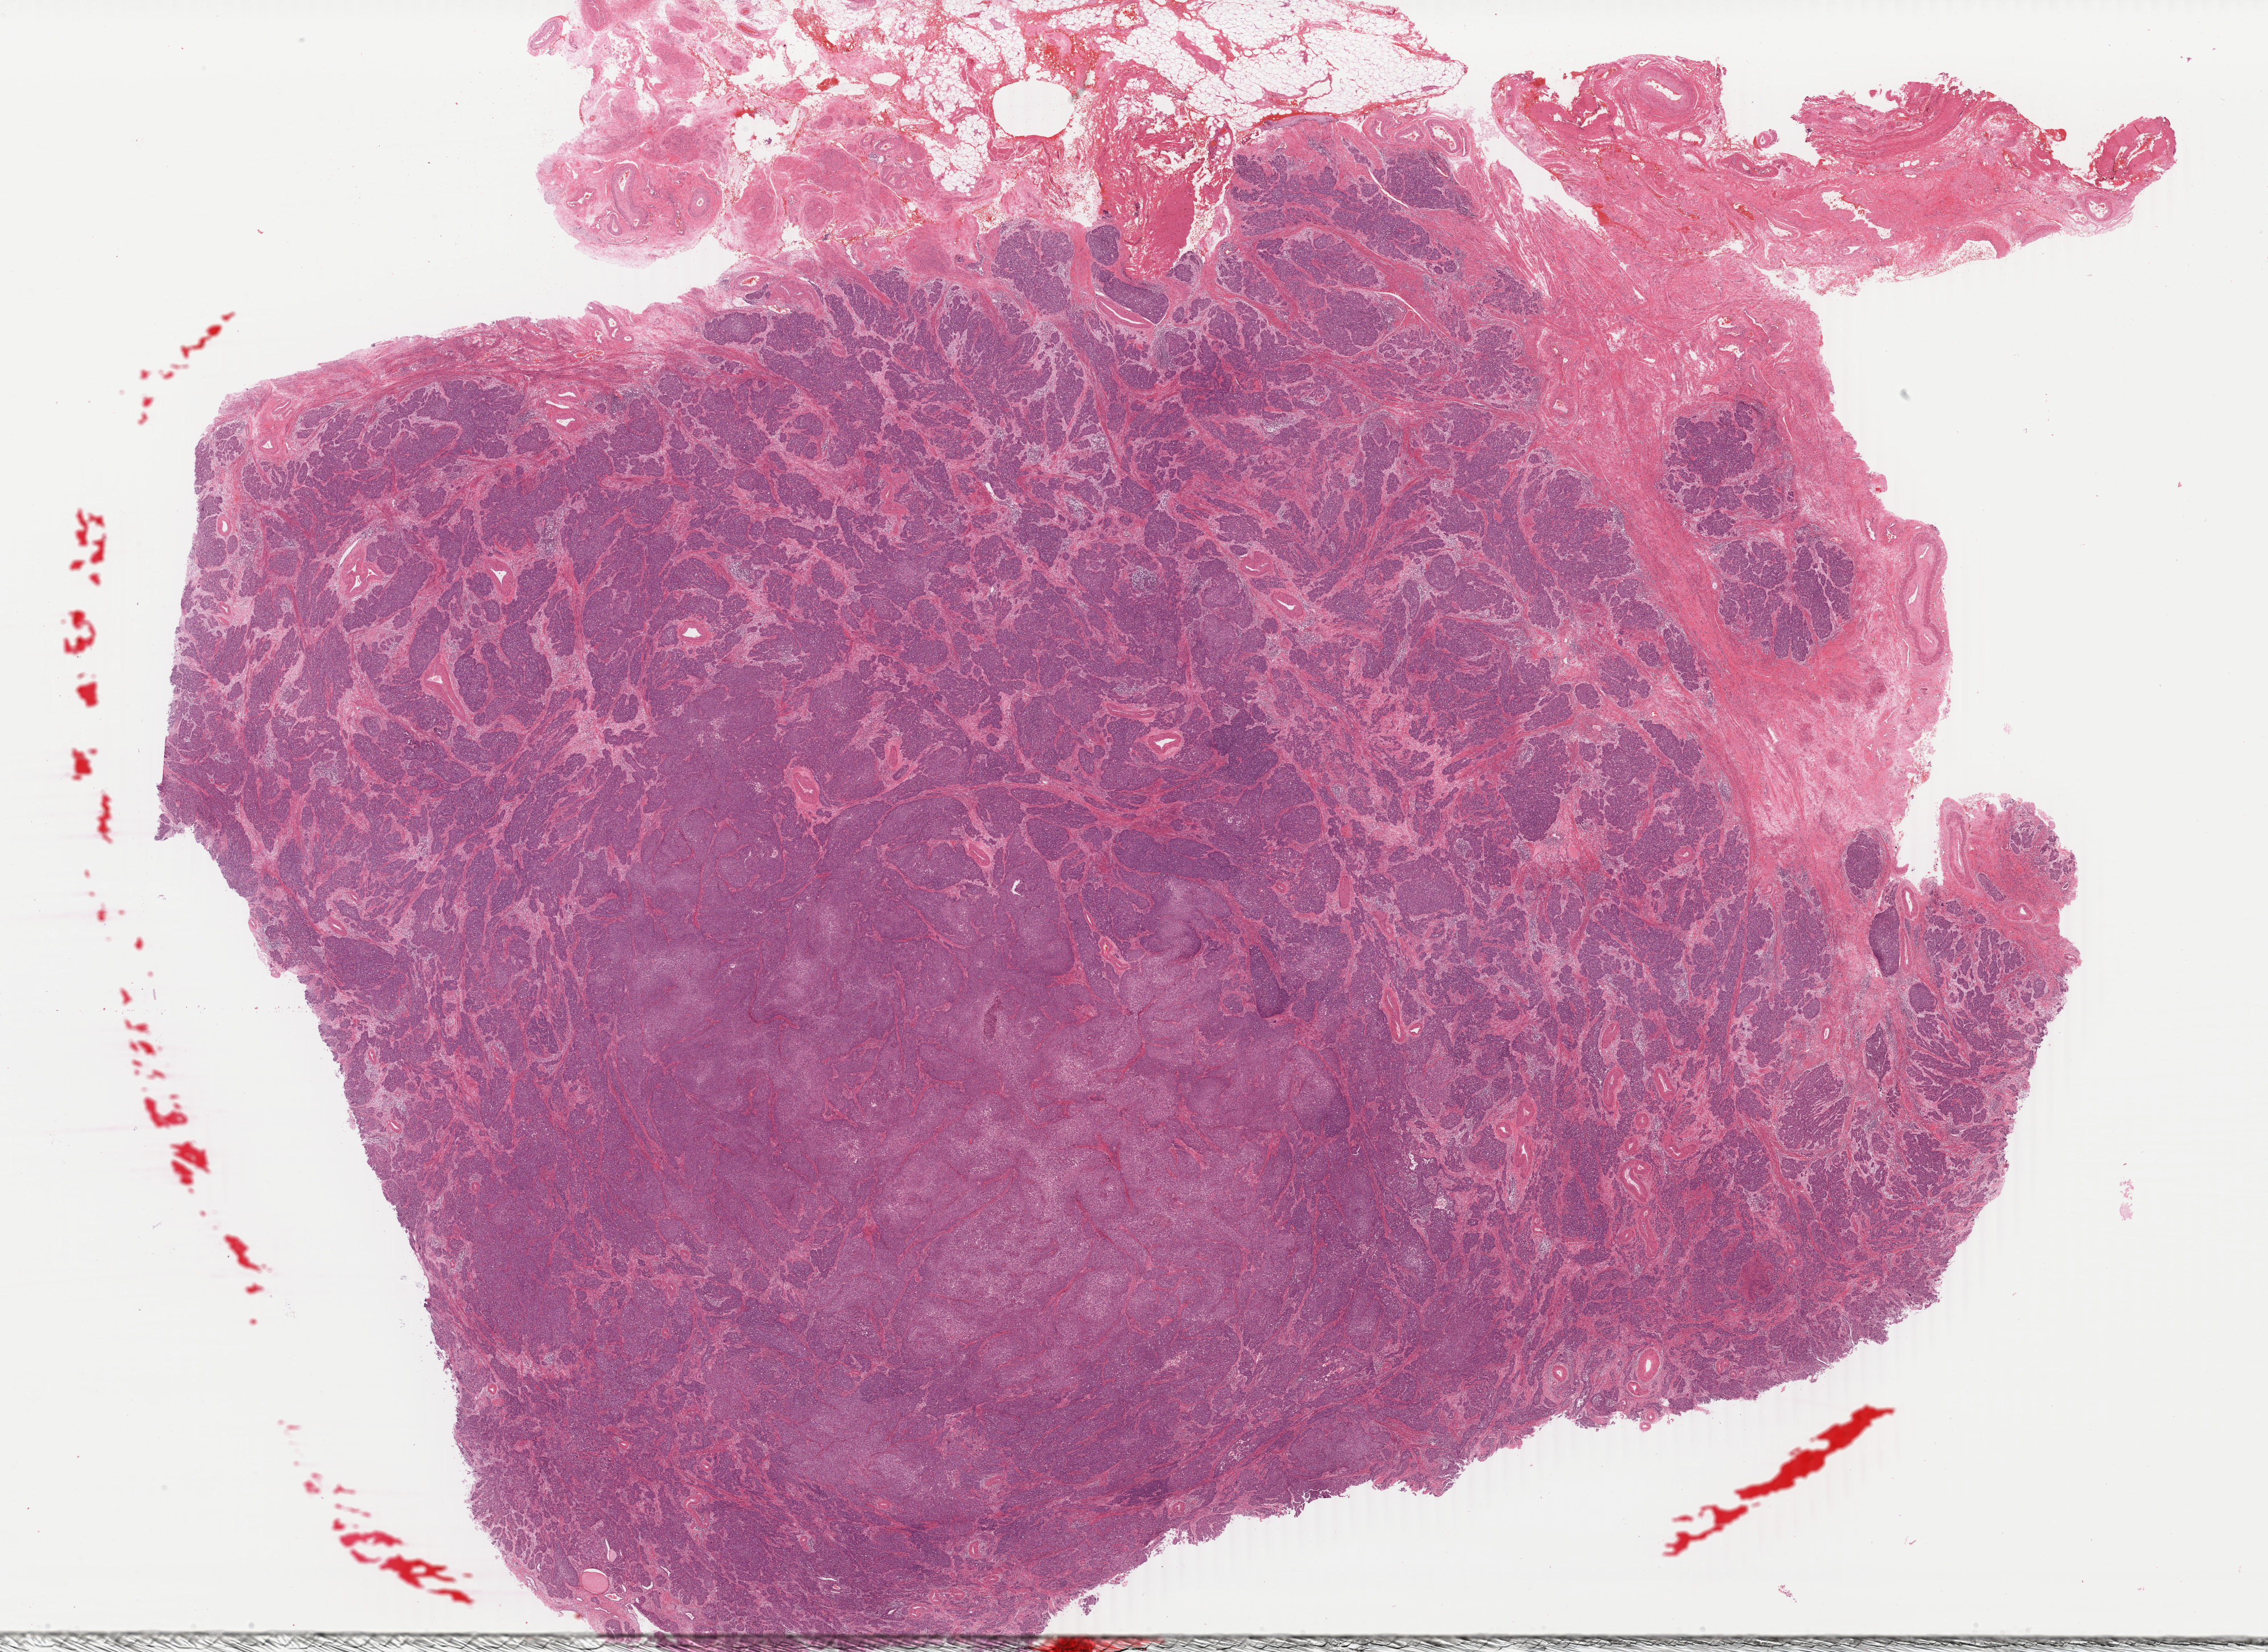
Digitized Hematoxylin and eosin (H&E) stained tissue section (whole slide) — low-resolution overview of the scanned area, about 31.6 x 23.1 mm. Formalin-fixed paraffin-embedded (FFPE) diagnostic section. Primary tumour sample from the cervix. Patient: female, age at initial diagnosis 54 years. Histologic grade: G3 (poorly differentiated).
FIGO stage: IB1. Pathologic diagnosis: Squamous cell carcinoma, NOS (cervix uteri).